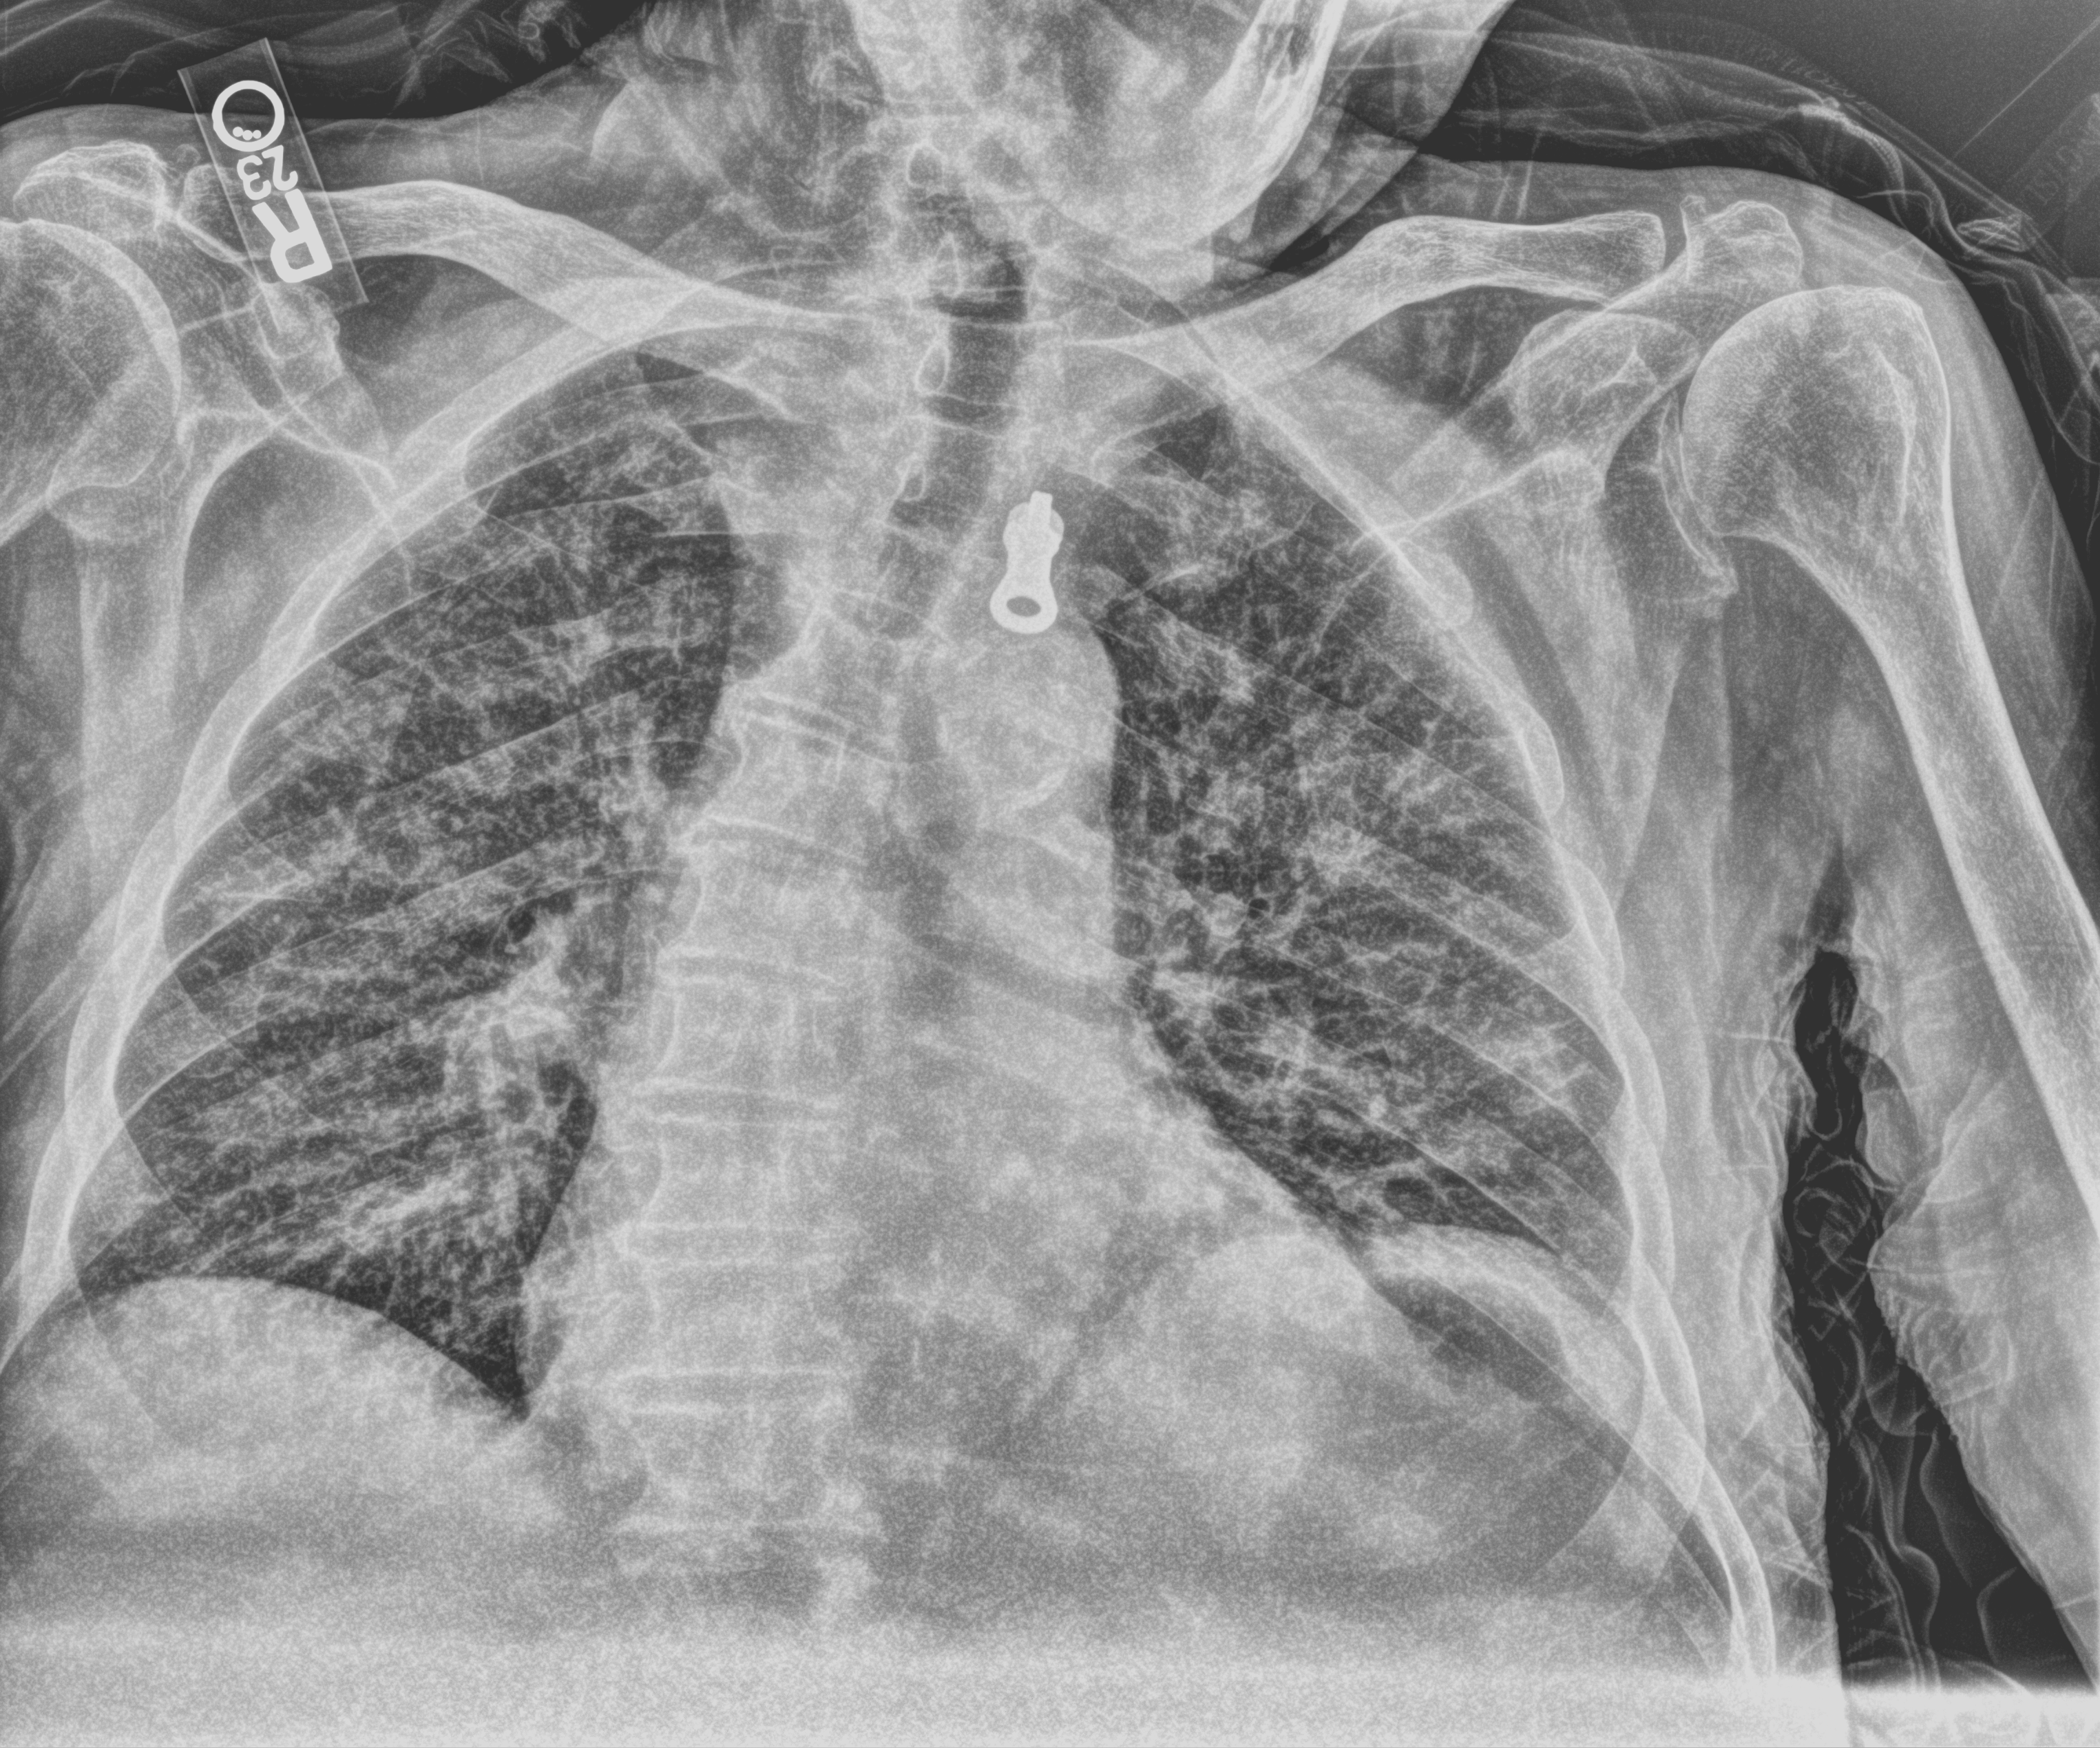
Bedside chest radiograph (computed radiography). Patient hospitalised with COVID-19; male, aged 75–90 years.
From the hospital-stay record, not from the radiograph (when in the stay this image was taken is not recorded): admitted to intensive care during this hospital stay: no.